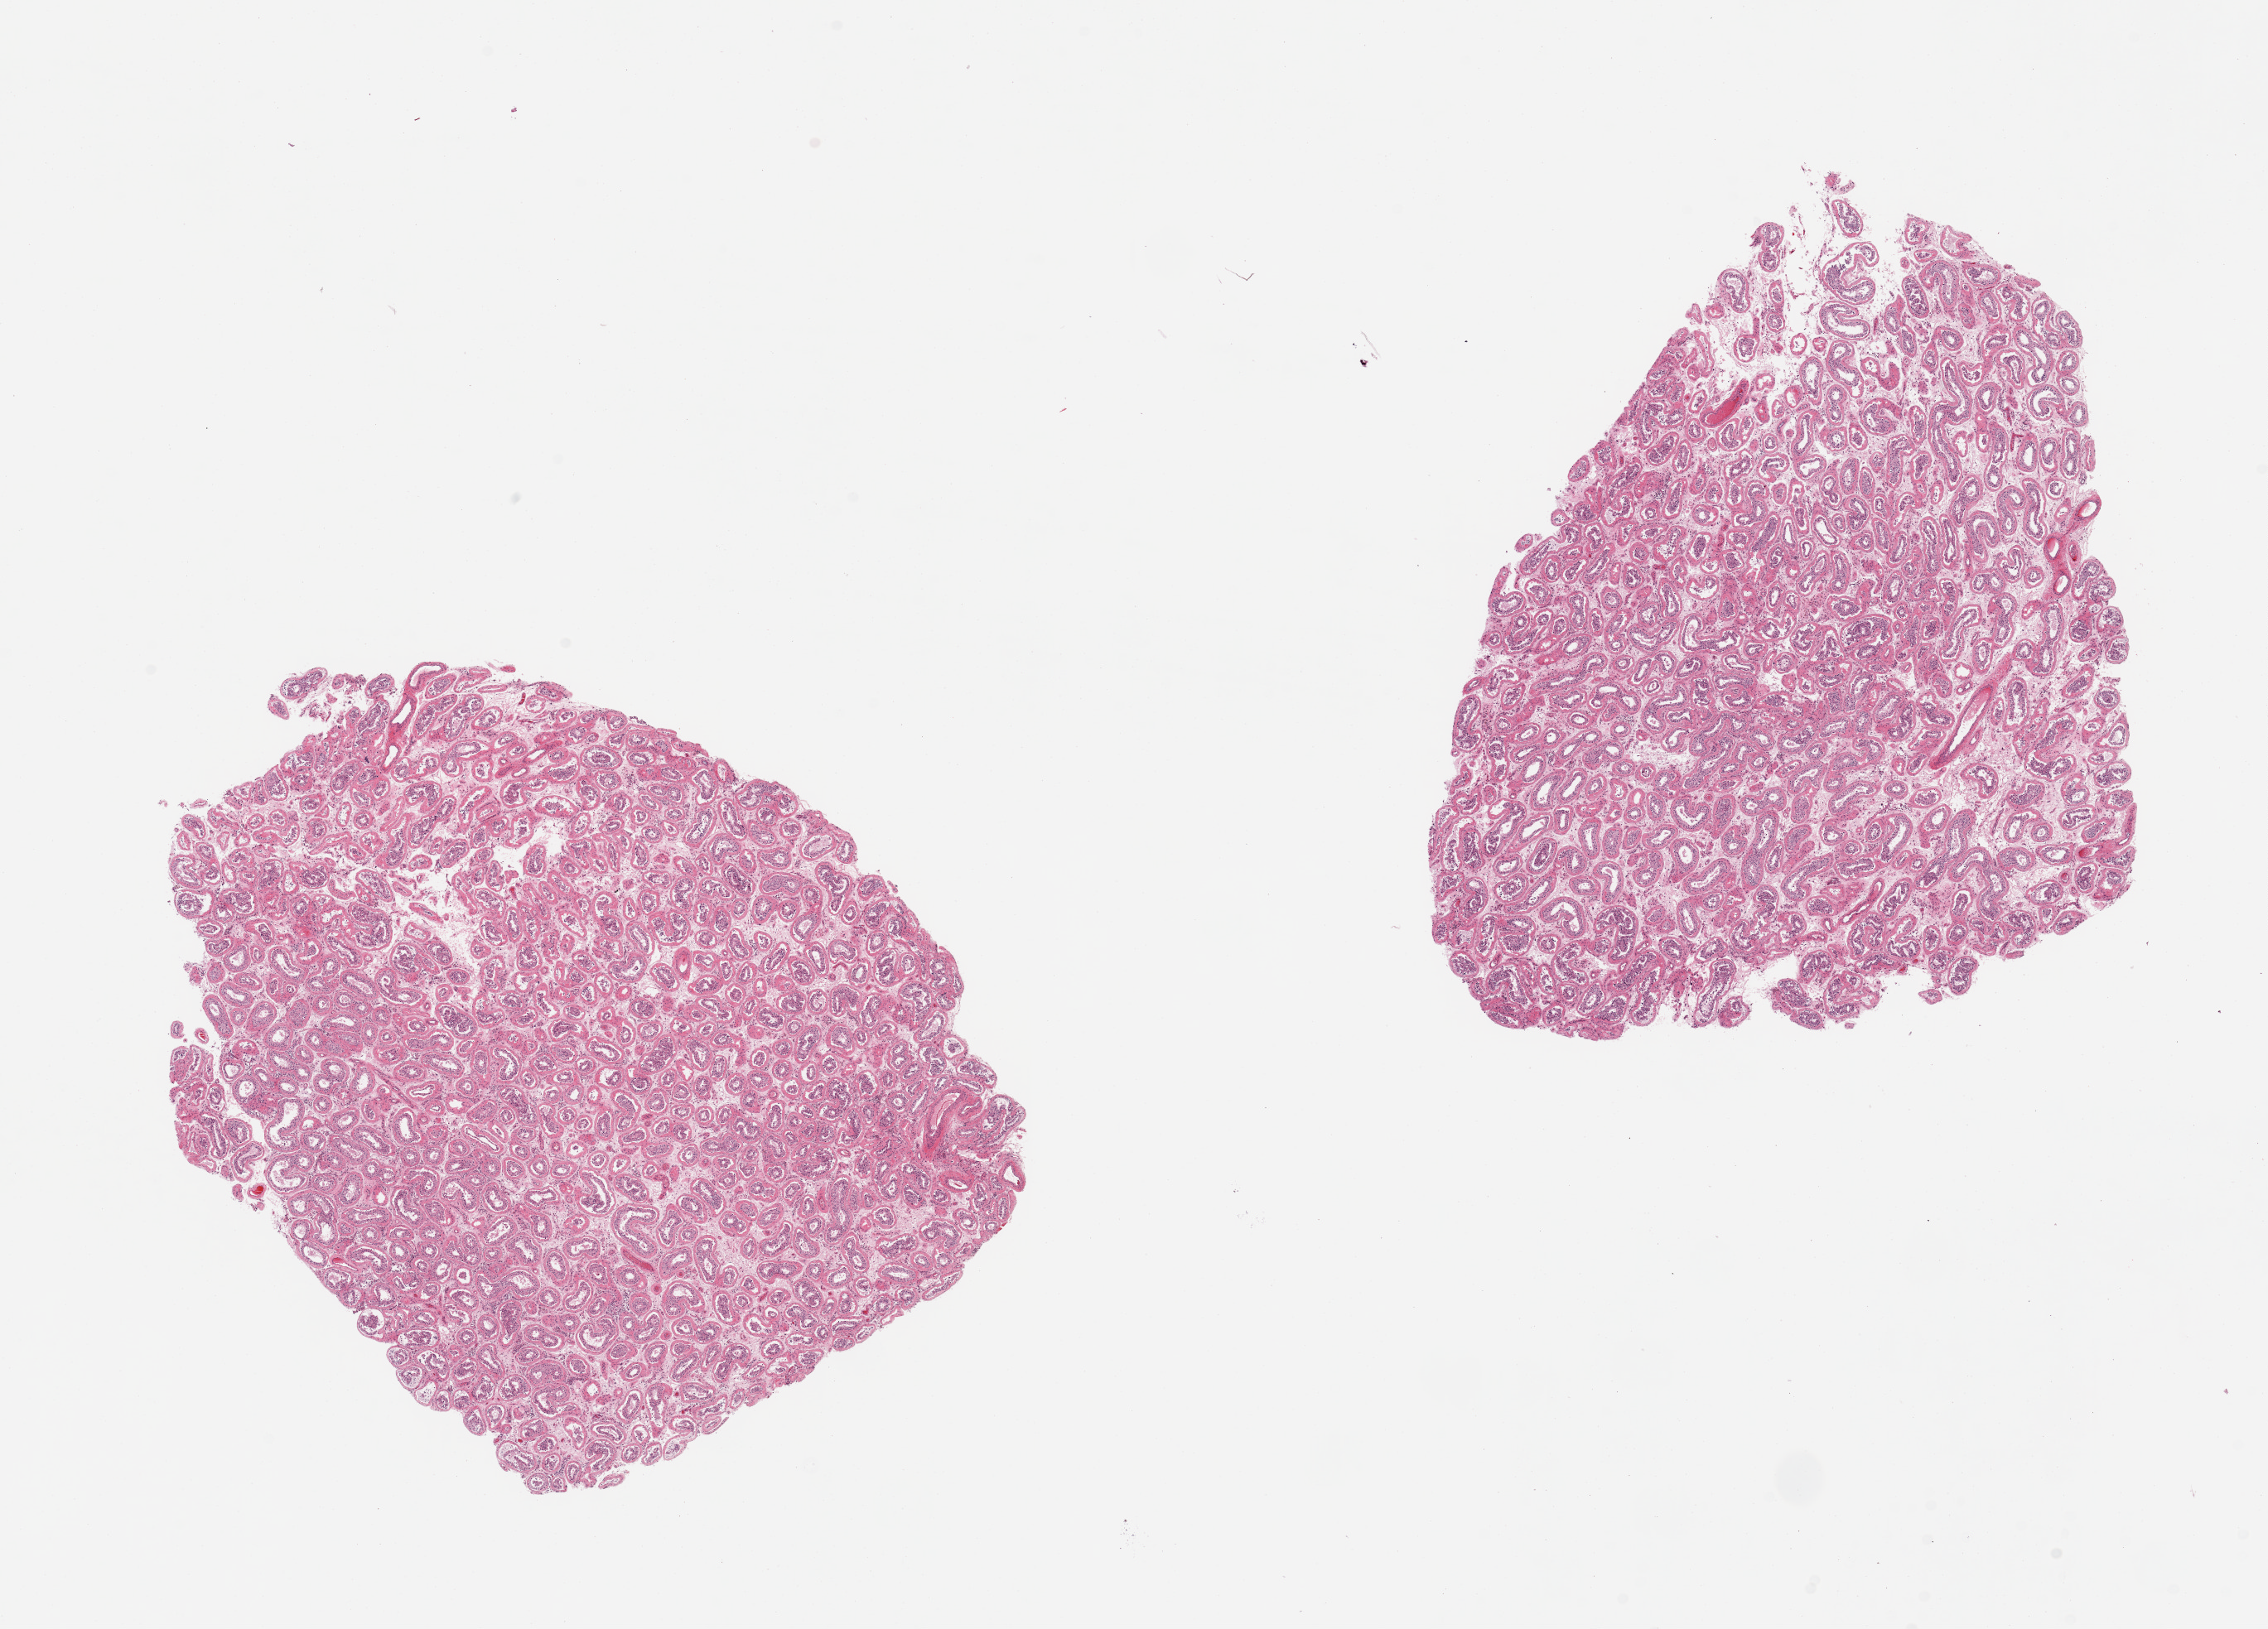
Digitized H&E-stained section — whole scanned area (about 21.7 x 15.6 mm) shown as a low-resolution overview; PAXgene-fixed, paraffin-embedded tissue; section of testis (target tissue); donor tissue sample. Male donor.
Reviewer comment on this tissue sample: 2 pieces. No spermatogenesis; mostly Sertoli cells.